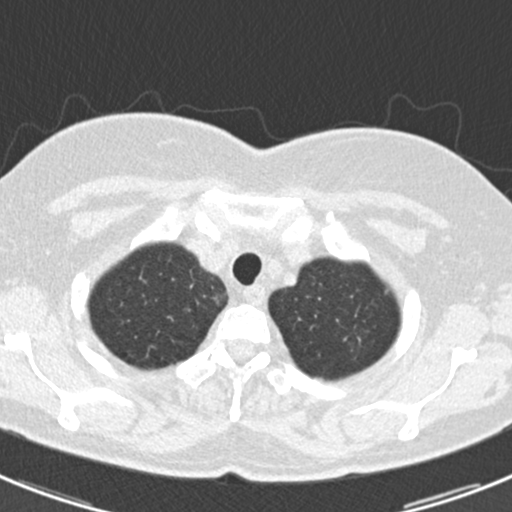
Axial slice from a low-dose chest CT screening exam. Baseline annual screen. Lung window (W 1500 / L -600 HU). 2 mm slice thickness. Slice 28 of 184 in the series. Female participant, aged 60 years at enrolment. Current smoker at enrolment.
- Lesion marked by an expert reader, bounding box (x1, y1, x2, y2) in pixels: (336, 313, 390, 365).
- The screening reader recorded 3 non-calcified nodules or masses ≥4 mm on this exam (lingula, left lower lobe, lingula); which of them this box marks is not recorded.
- Participant outcome: lung cancer diagnosed 886 days after this screen (after the third annual screen) — non-small cell carcinoma, left upper lobe, poorly differentiated (G3), stage IB (AJCC 6th edition), 7 mm at pathology.